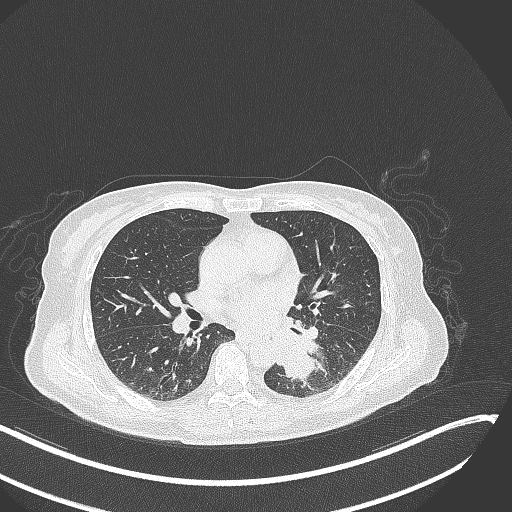
Chest CT, one axial slice; lung window (W 1500 / L -600 HU); 512 × 512 image matrix, field of view 400 × 400 mm. Patient: female, 64 years. From the clinical record (not read from this slice): clinical TNM (as recorded): T3 N1 M1.
Outlined on this slice (bounding box drawn by a radiologist):
- lung tumour (recorded histology: small cell carcinoma): bounding box [x1, y1, x2, y2] px = [270, 325, 326, 387]